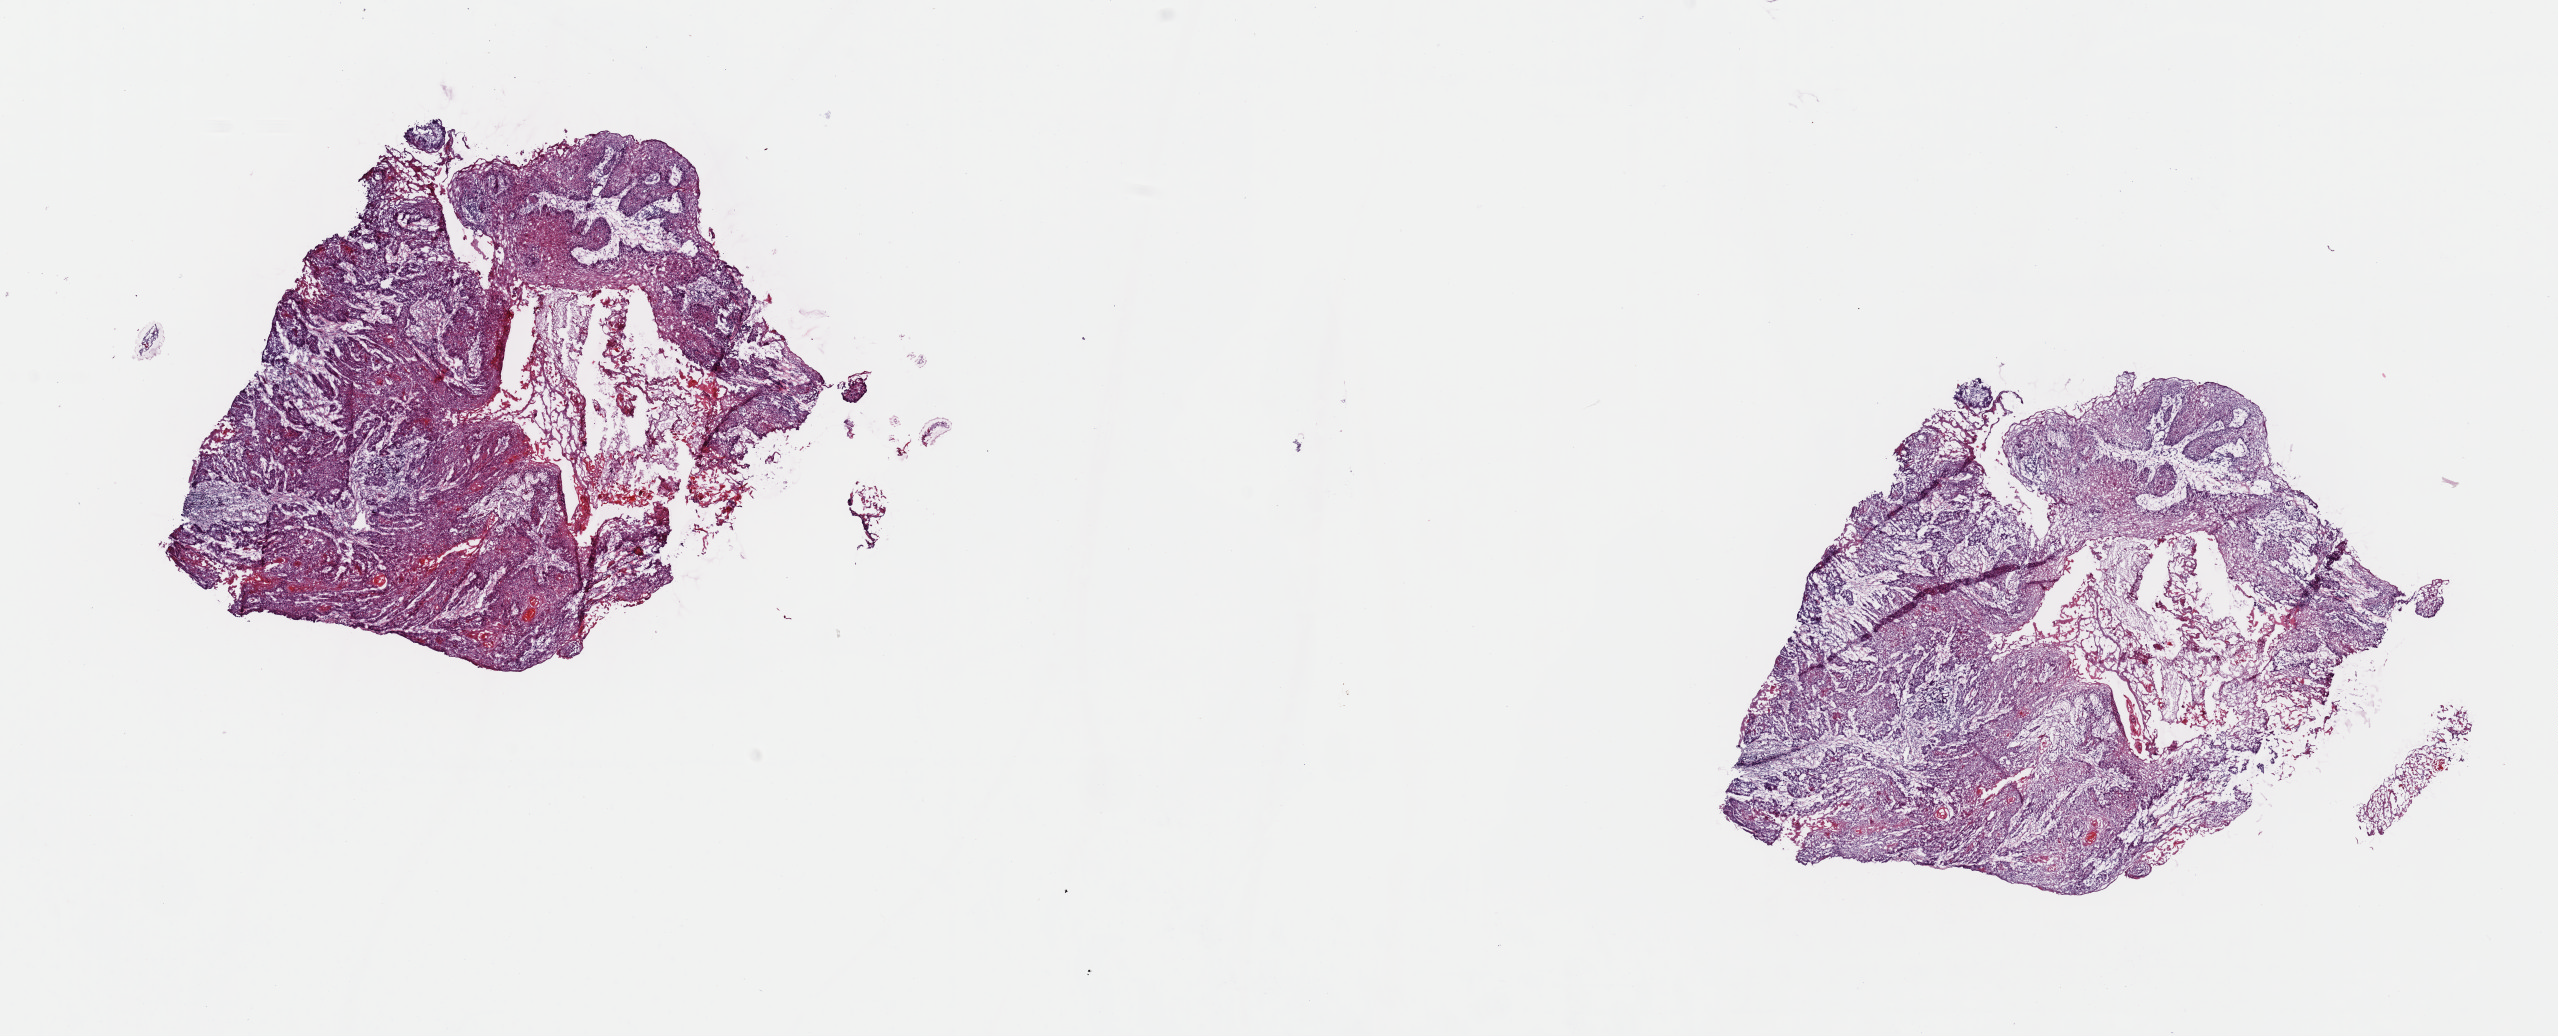
Digitized H&E tissue section (whole slide), low-resolution overview of the scanned area, about 20.2 x 8.2 mm, frozen section from the top of the tissue portion, sample: primary tumour, head and neck. Patient: female, age at initial diagnosis 61 years. Histologic grade: G1 (well differentiated). Pathologist review of this section (percent, as recorded): tumour cells 90%, tumour nuclei 90%, normal cells 0%, stromal cells 10%, necrosis 0%. Inflammatory infiltration, as recorded: lymphocyte infiltration 5%, monocyte infiltration 0%, neutrophil infiltration 0%.
- AJCC pathologic stage: III
- pathologic diagnosis: Squamous cell carcinoma, keratinizing, NOS (tongue, NOS)